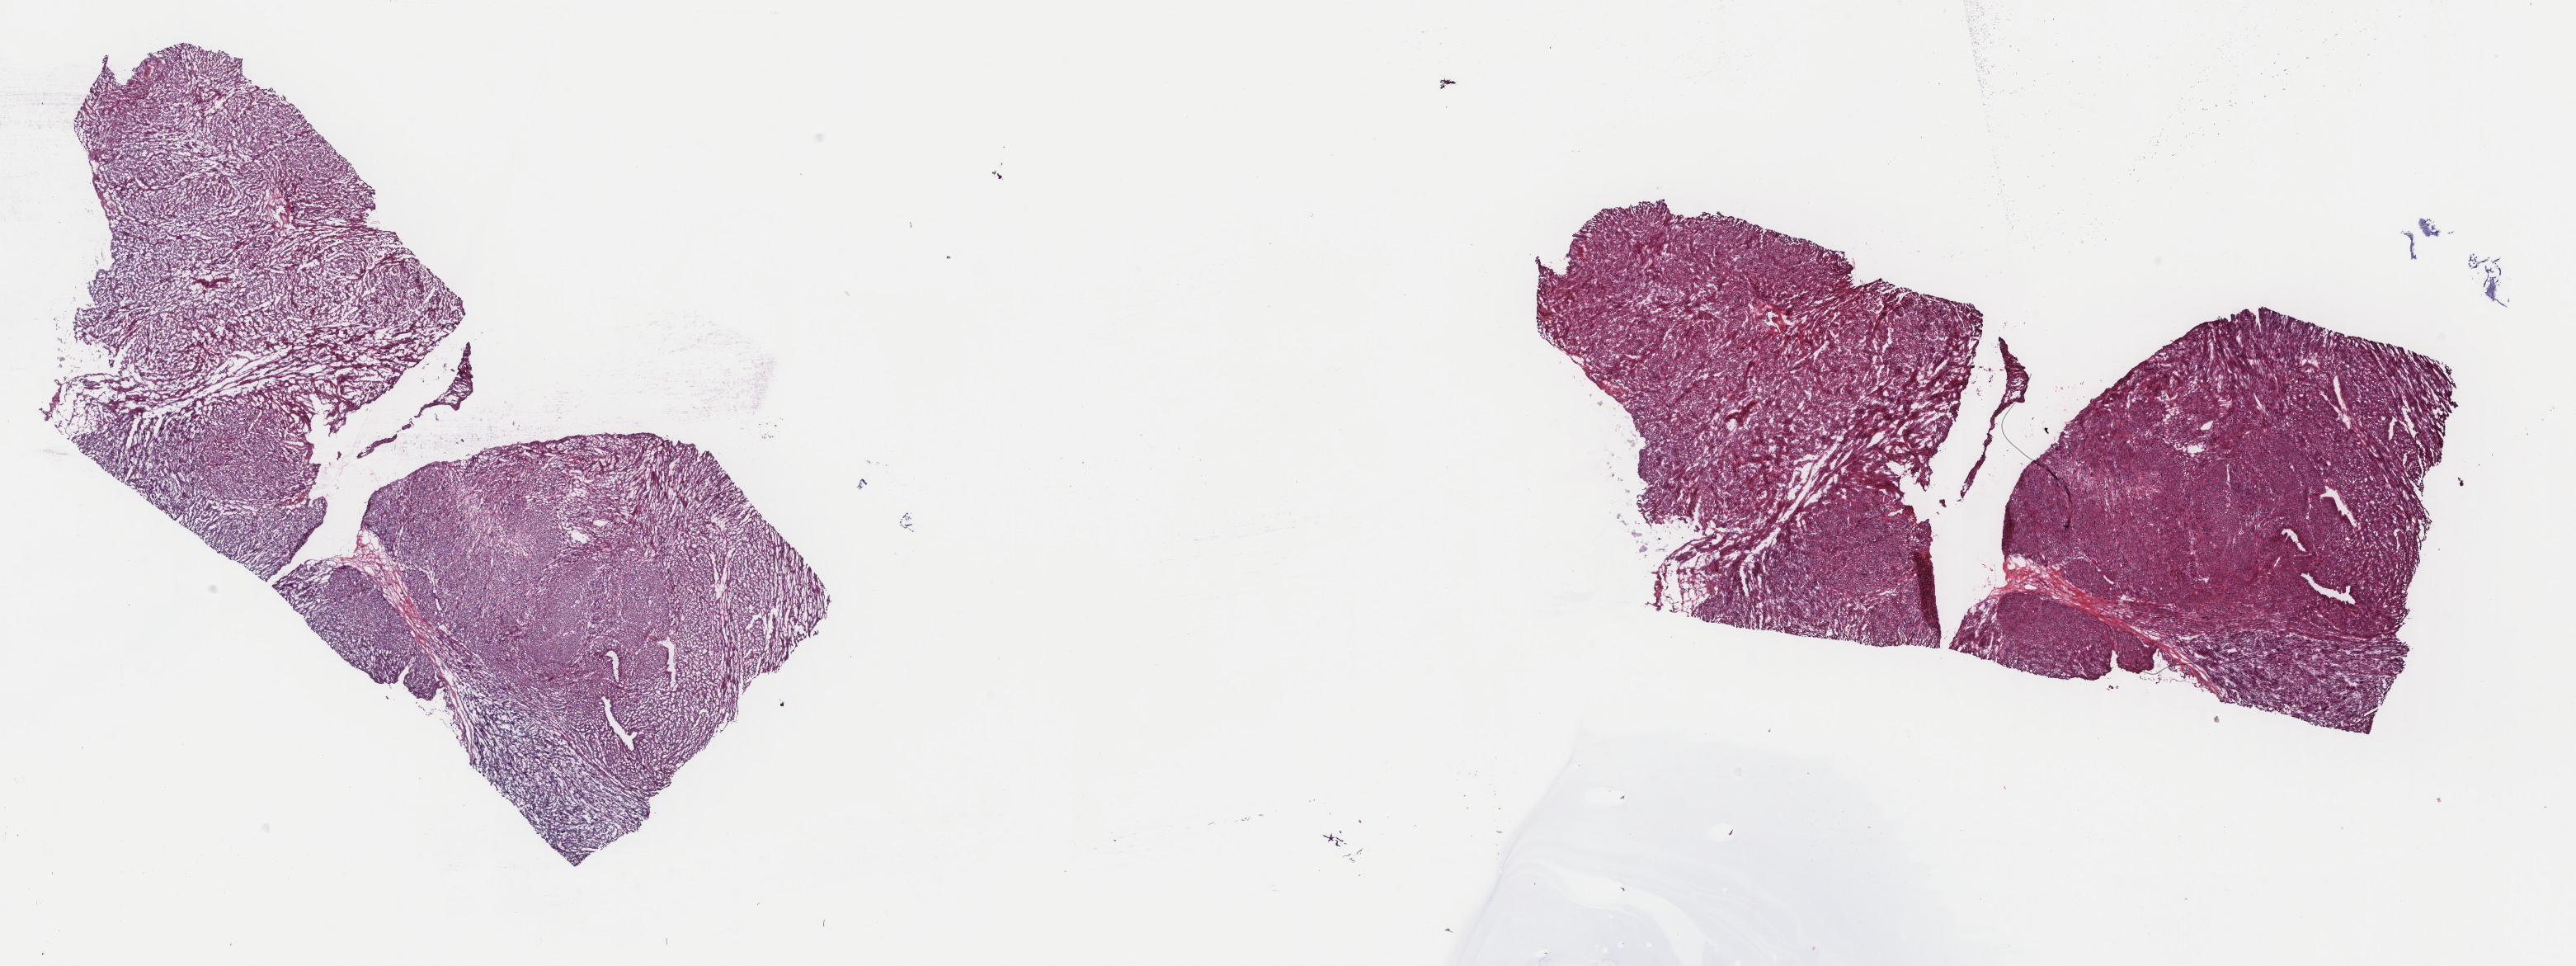
Whole-slide histology image, H&E-stained, a low-resolution overview of the entire scanned area, about 24.8 x 9.3 mm (acquisition: 40x scan); frozen section; retroperitoneum and peritoneum, primary tumour sample. Patient: male, age at initial diagnosis 78 years. Composition of this section per pathologist review: tumour cells 80%, tumour nuclei 80%.
Pathologic diagnosis: Leiomyosarcoma, NOS (retroperitoneum).